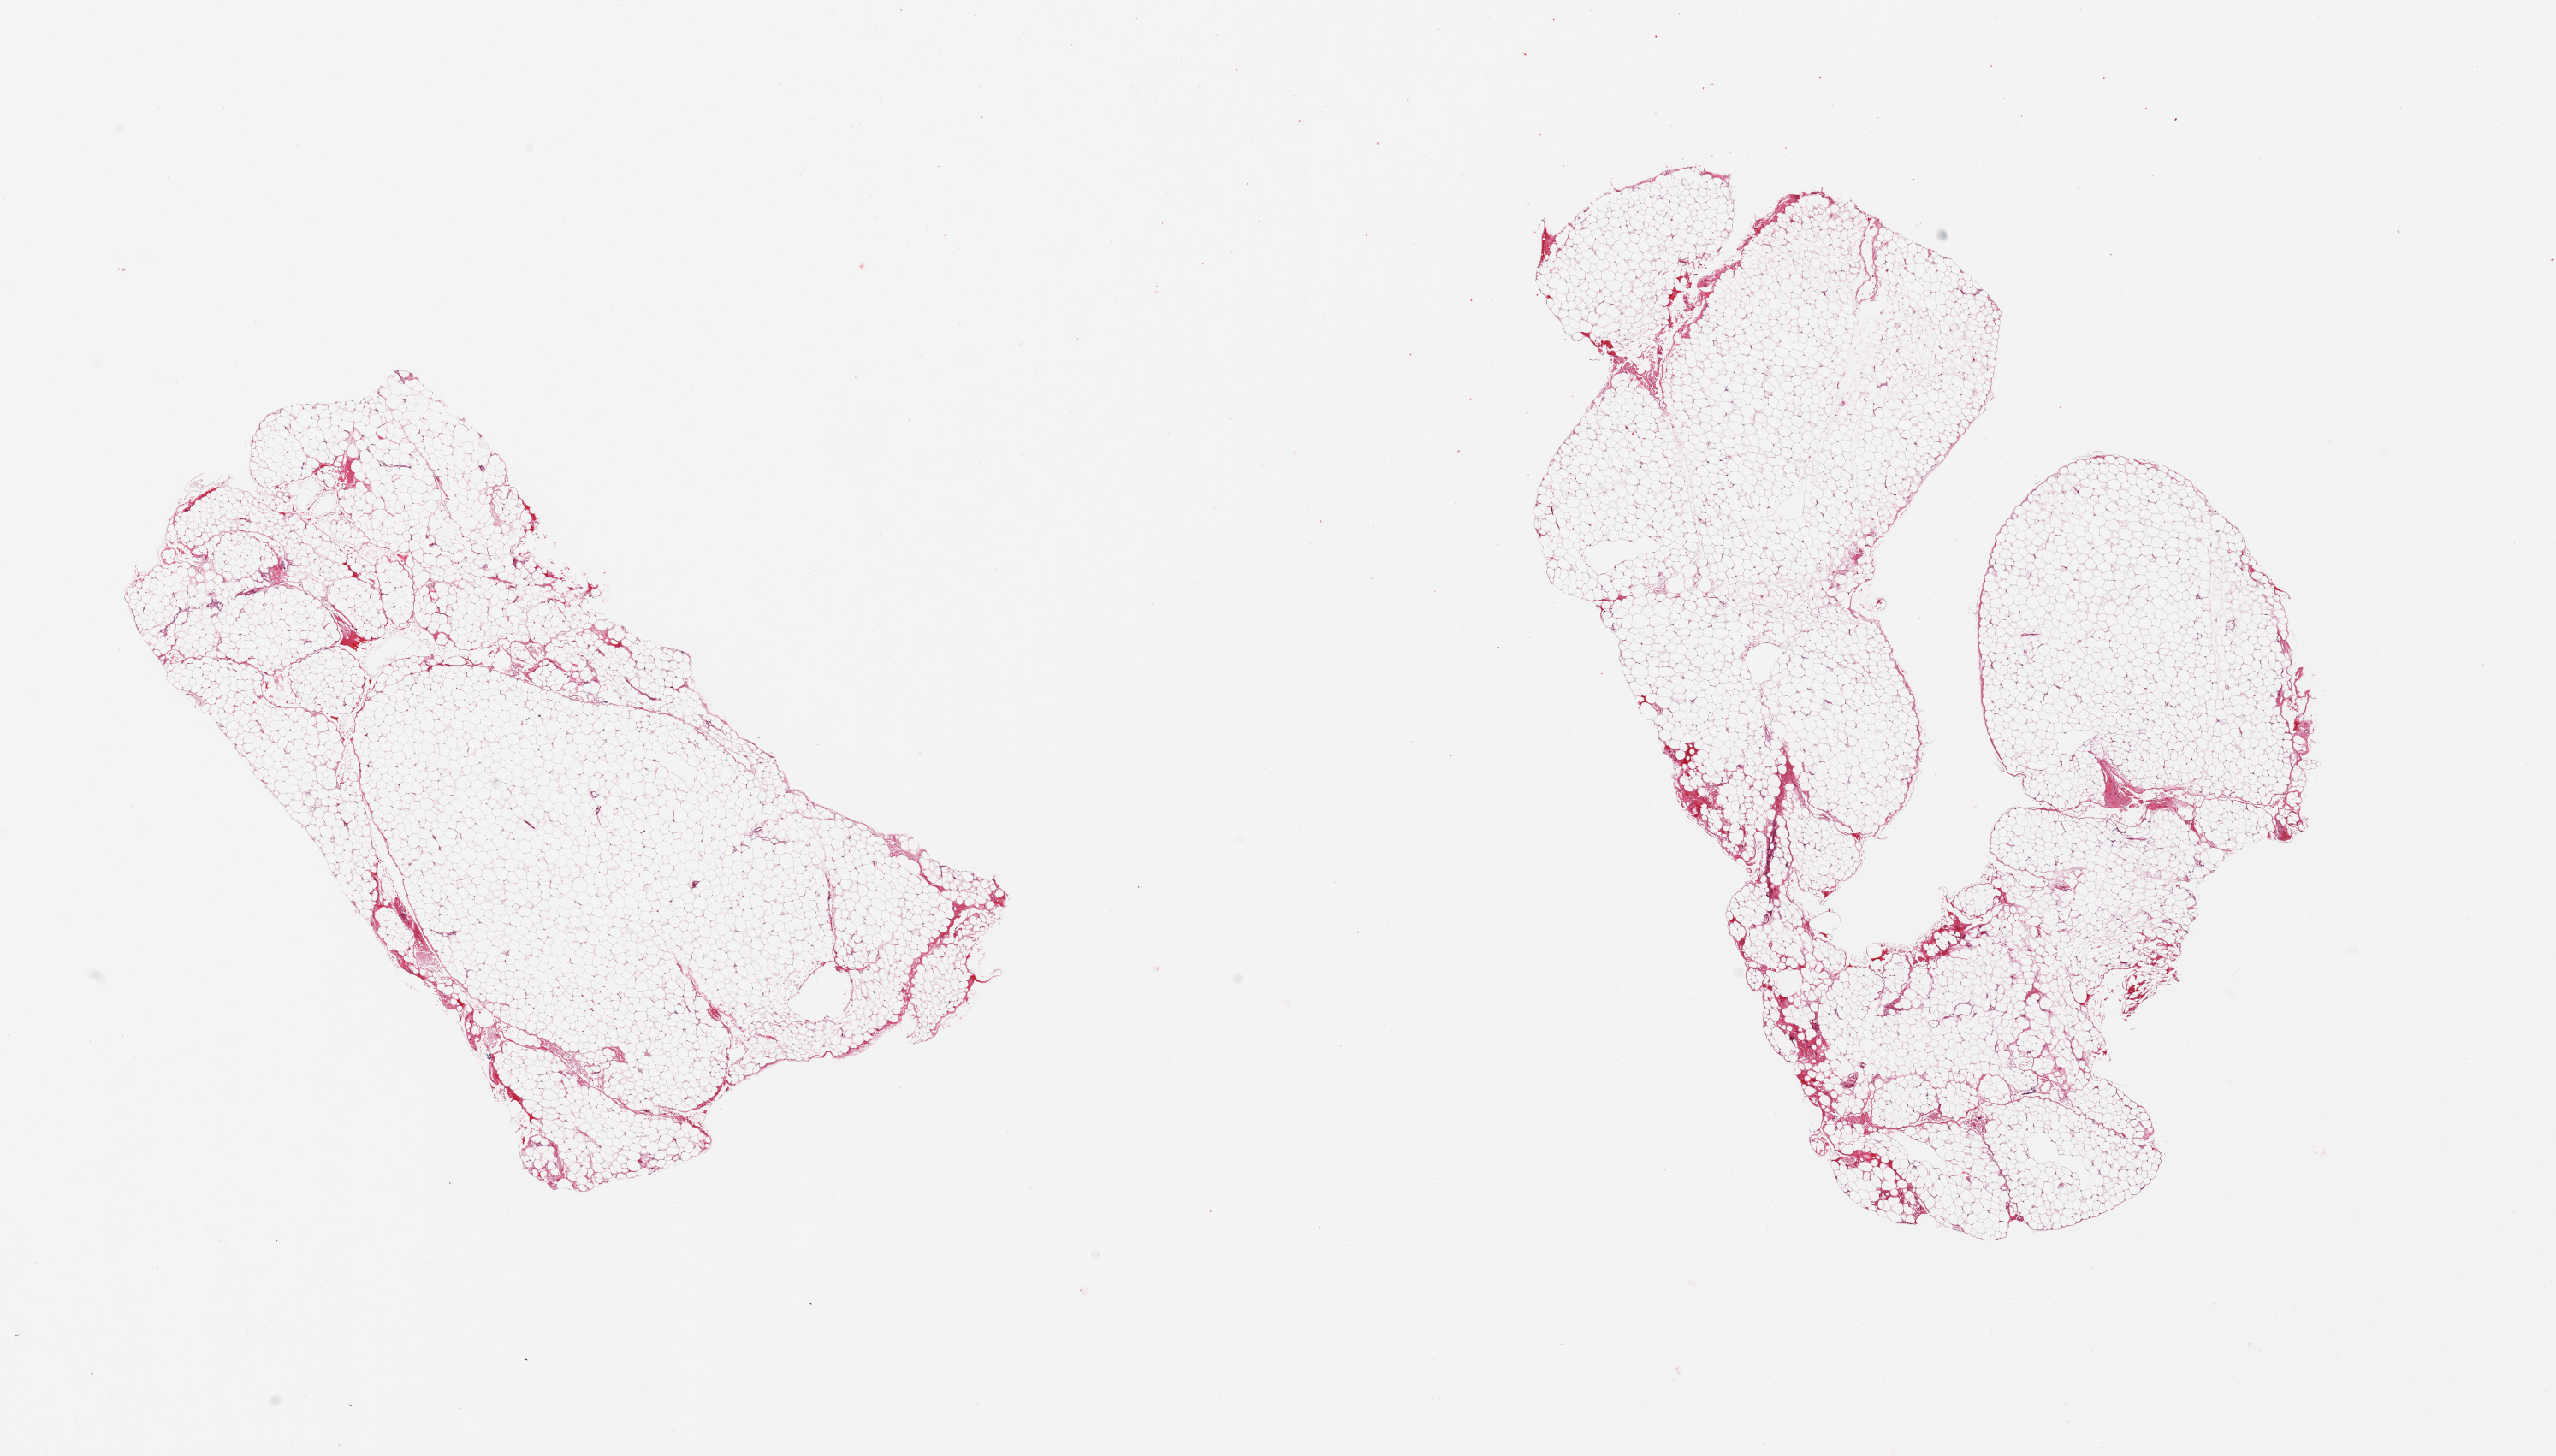
Whole-slide image, H&E stain — low-resolution overview of the scanned area, about 23.6 x 13.5 mm (from a 20x scan); PAXgene-fixed, paraffin-embedded tissue; target tissue: omentum; tissue donor sample. Male donor.
* reviewer comment on this tissue sample: 2 pieces; minimal fibrous content